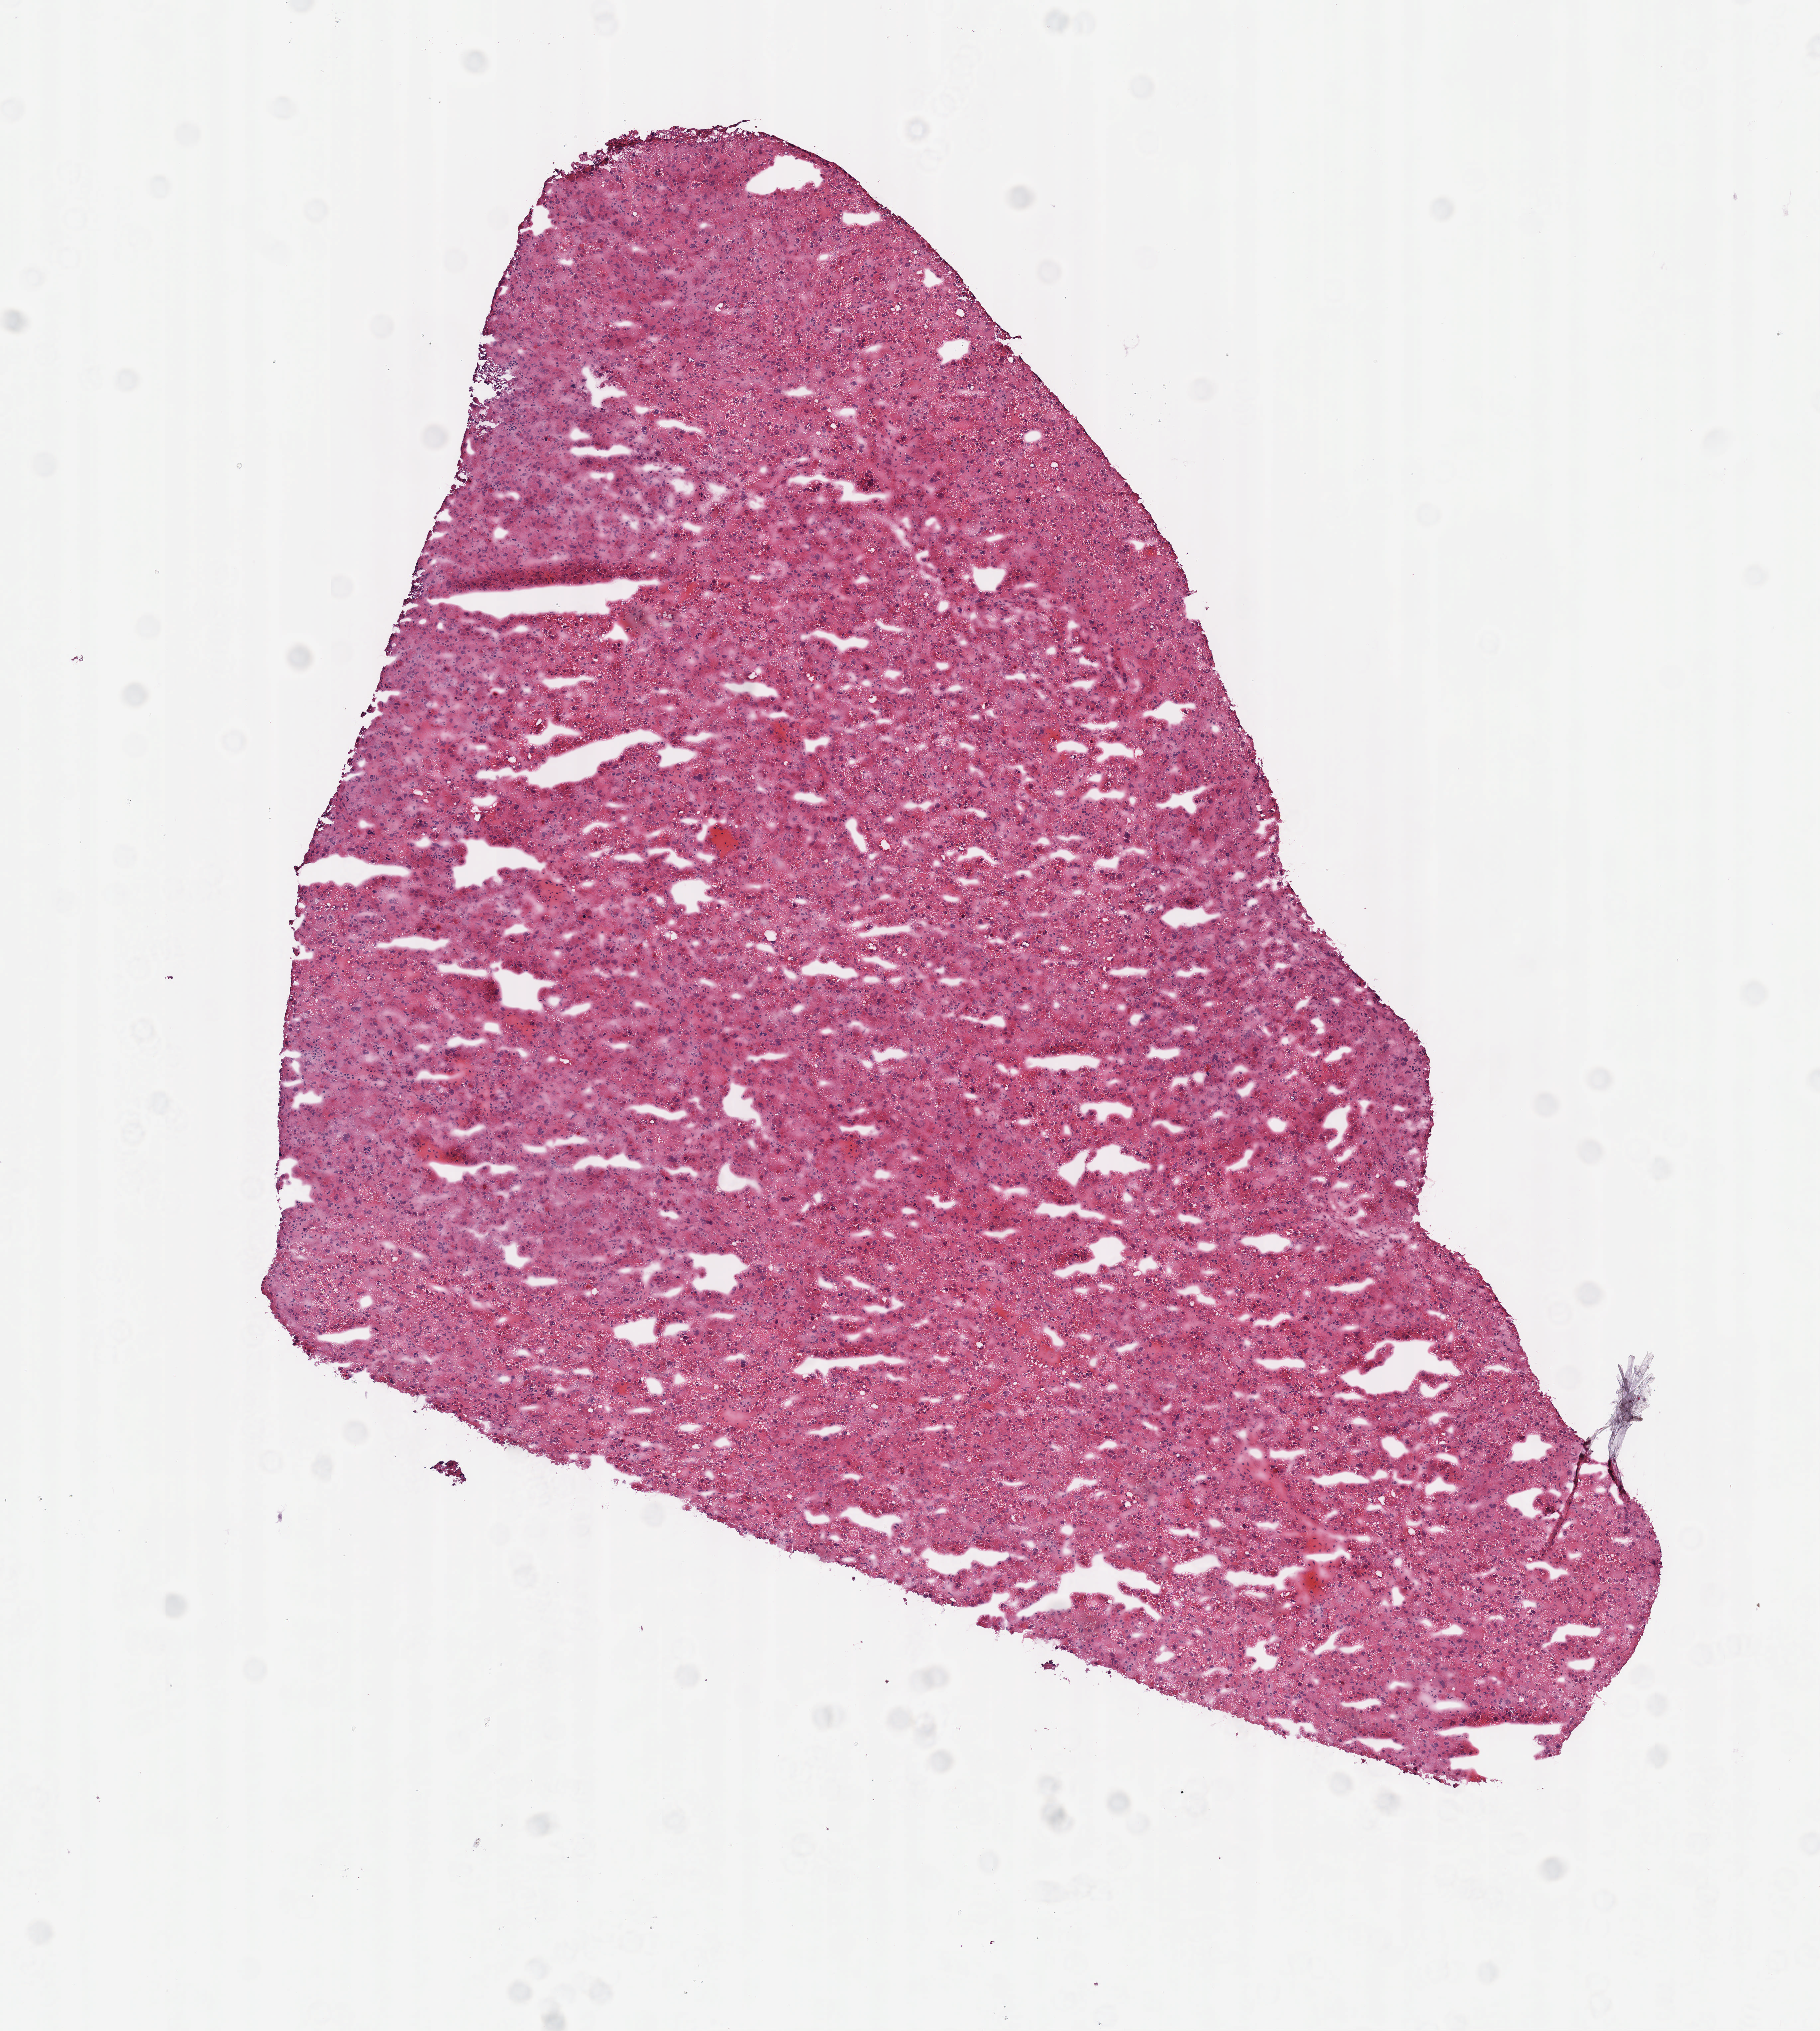
Digitized H&E tissue section (whole slide) — shown as a low-resolution overview of the whole scanned area (about 5.5 x 6.2 mm, from a 40x scan); frozen section from the top of the tissue portion; liver, primary tumour sample. Patient: male, age at initial diagnosis 72 years. Histologic grade: G2 (moderately differentiated). Pathologist review of this section (percent, as recorded): tumour cells 100%, tumour nuclei 80%, normal cells 0%, stromal cells 0%, necrosis 0%. Inflammatory infiltration, as recorded: lymphocyte infiltration 3%, monocyte infiltration 0%, neutrophil infiltration 0%.
- TNM: T1 N0 M0
- AJCC pathologic stage: I (7th edition)
- pathologic diagnosis: Hepatocellular carcinoma, NOS